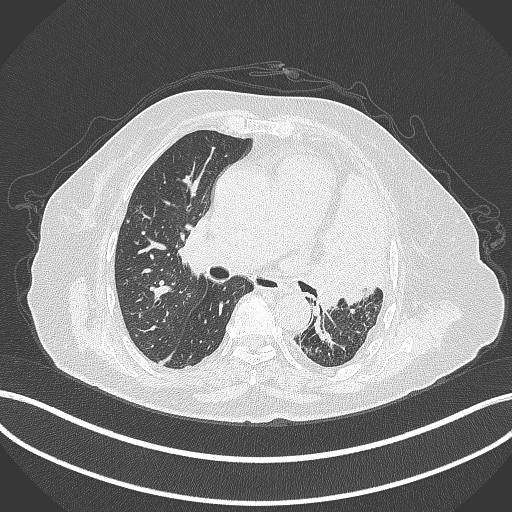
Chest CT, one axial slice. Slice 216 of 399 in the series (ordered by position). 120 kVp. Lung window (W 1500 / L -600 HU). 1 mm slice thickness. 512 × 512 image matrix, field of view 400 × 400 mm. Female patient, age 75 years. Case-level facts recorded for this patient, not image findings: clinical TNM (as recorded): T3 N3 M1.
Annotated regions visible in this slice (bounding box drawn by a radiologist):
- lung tumour (recorded histology: adenocarcinoma): bounding box [x1, y1, x2, y2] px = [306, 162, 394, 314]